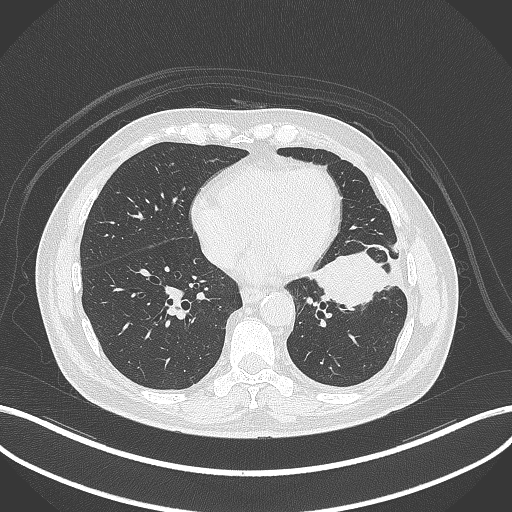
Chest CT, one axial slice. Slice 132 of 230 in the series (ordered by position). 120 kVp. Lung window (W 1500 / L -600 HU). 1 mm slice thickness. 512 × 512 image matrix, field of view 400 × 400 mm. Male patient, age 68 years. From the clinical record (not read from this slice): clinical TNM (as recorded): T2b N0 M0.
Annotated regions visible in this slice (bounding box drawn by a radiologist):
- lung tumour (recorded histology: squamous cell carcinoma): bounding box <305,250,391,310> (left, top, right, bottom; pixels)